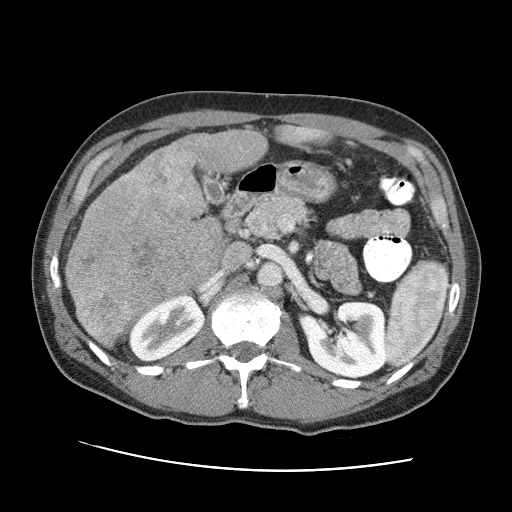
Contrast-enhanced abdominal CT (liver protocol), one axial slice; position 35 of 95 along the scan axis; 120 kVp; one of 2 acquisitions stored at this slice position; soft-tissue window (W 400 / L 40 HU); 2.5 mm slice thickness; 512 × 512 image matrix, field of view 360 × 360 mm. Case-level facts recorded for this patient, not image findings: diagnosis: hepatocellular carcinoma (patient treated with transarterial chemoembolisation; whether this scan precedes or follows treatment is not stated here); TNM stage (as recorded): Stage-IVA.
Structures marked on this image (semi-automatically segmented with operator editing):
- liver parenchyma outside the tumour (the mass and vessels are separate outlines, so this box may not span the whole liver): bounding box <64,126,307,310> (left, top, right, bottom; pixels)
- mass: <65,143,225,343>
- liver vessels: <296,128,307,137>